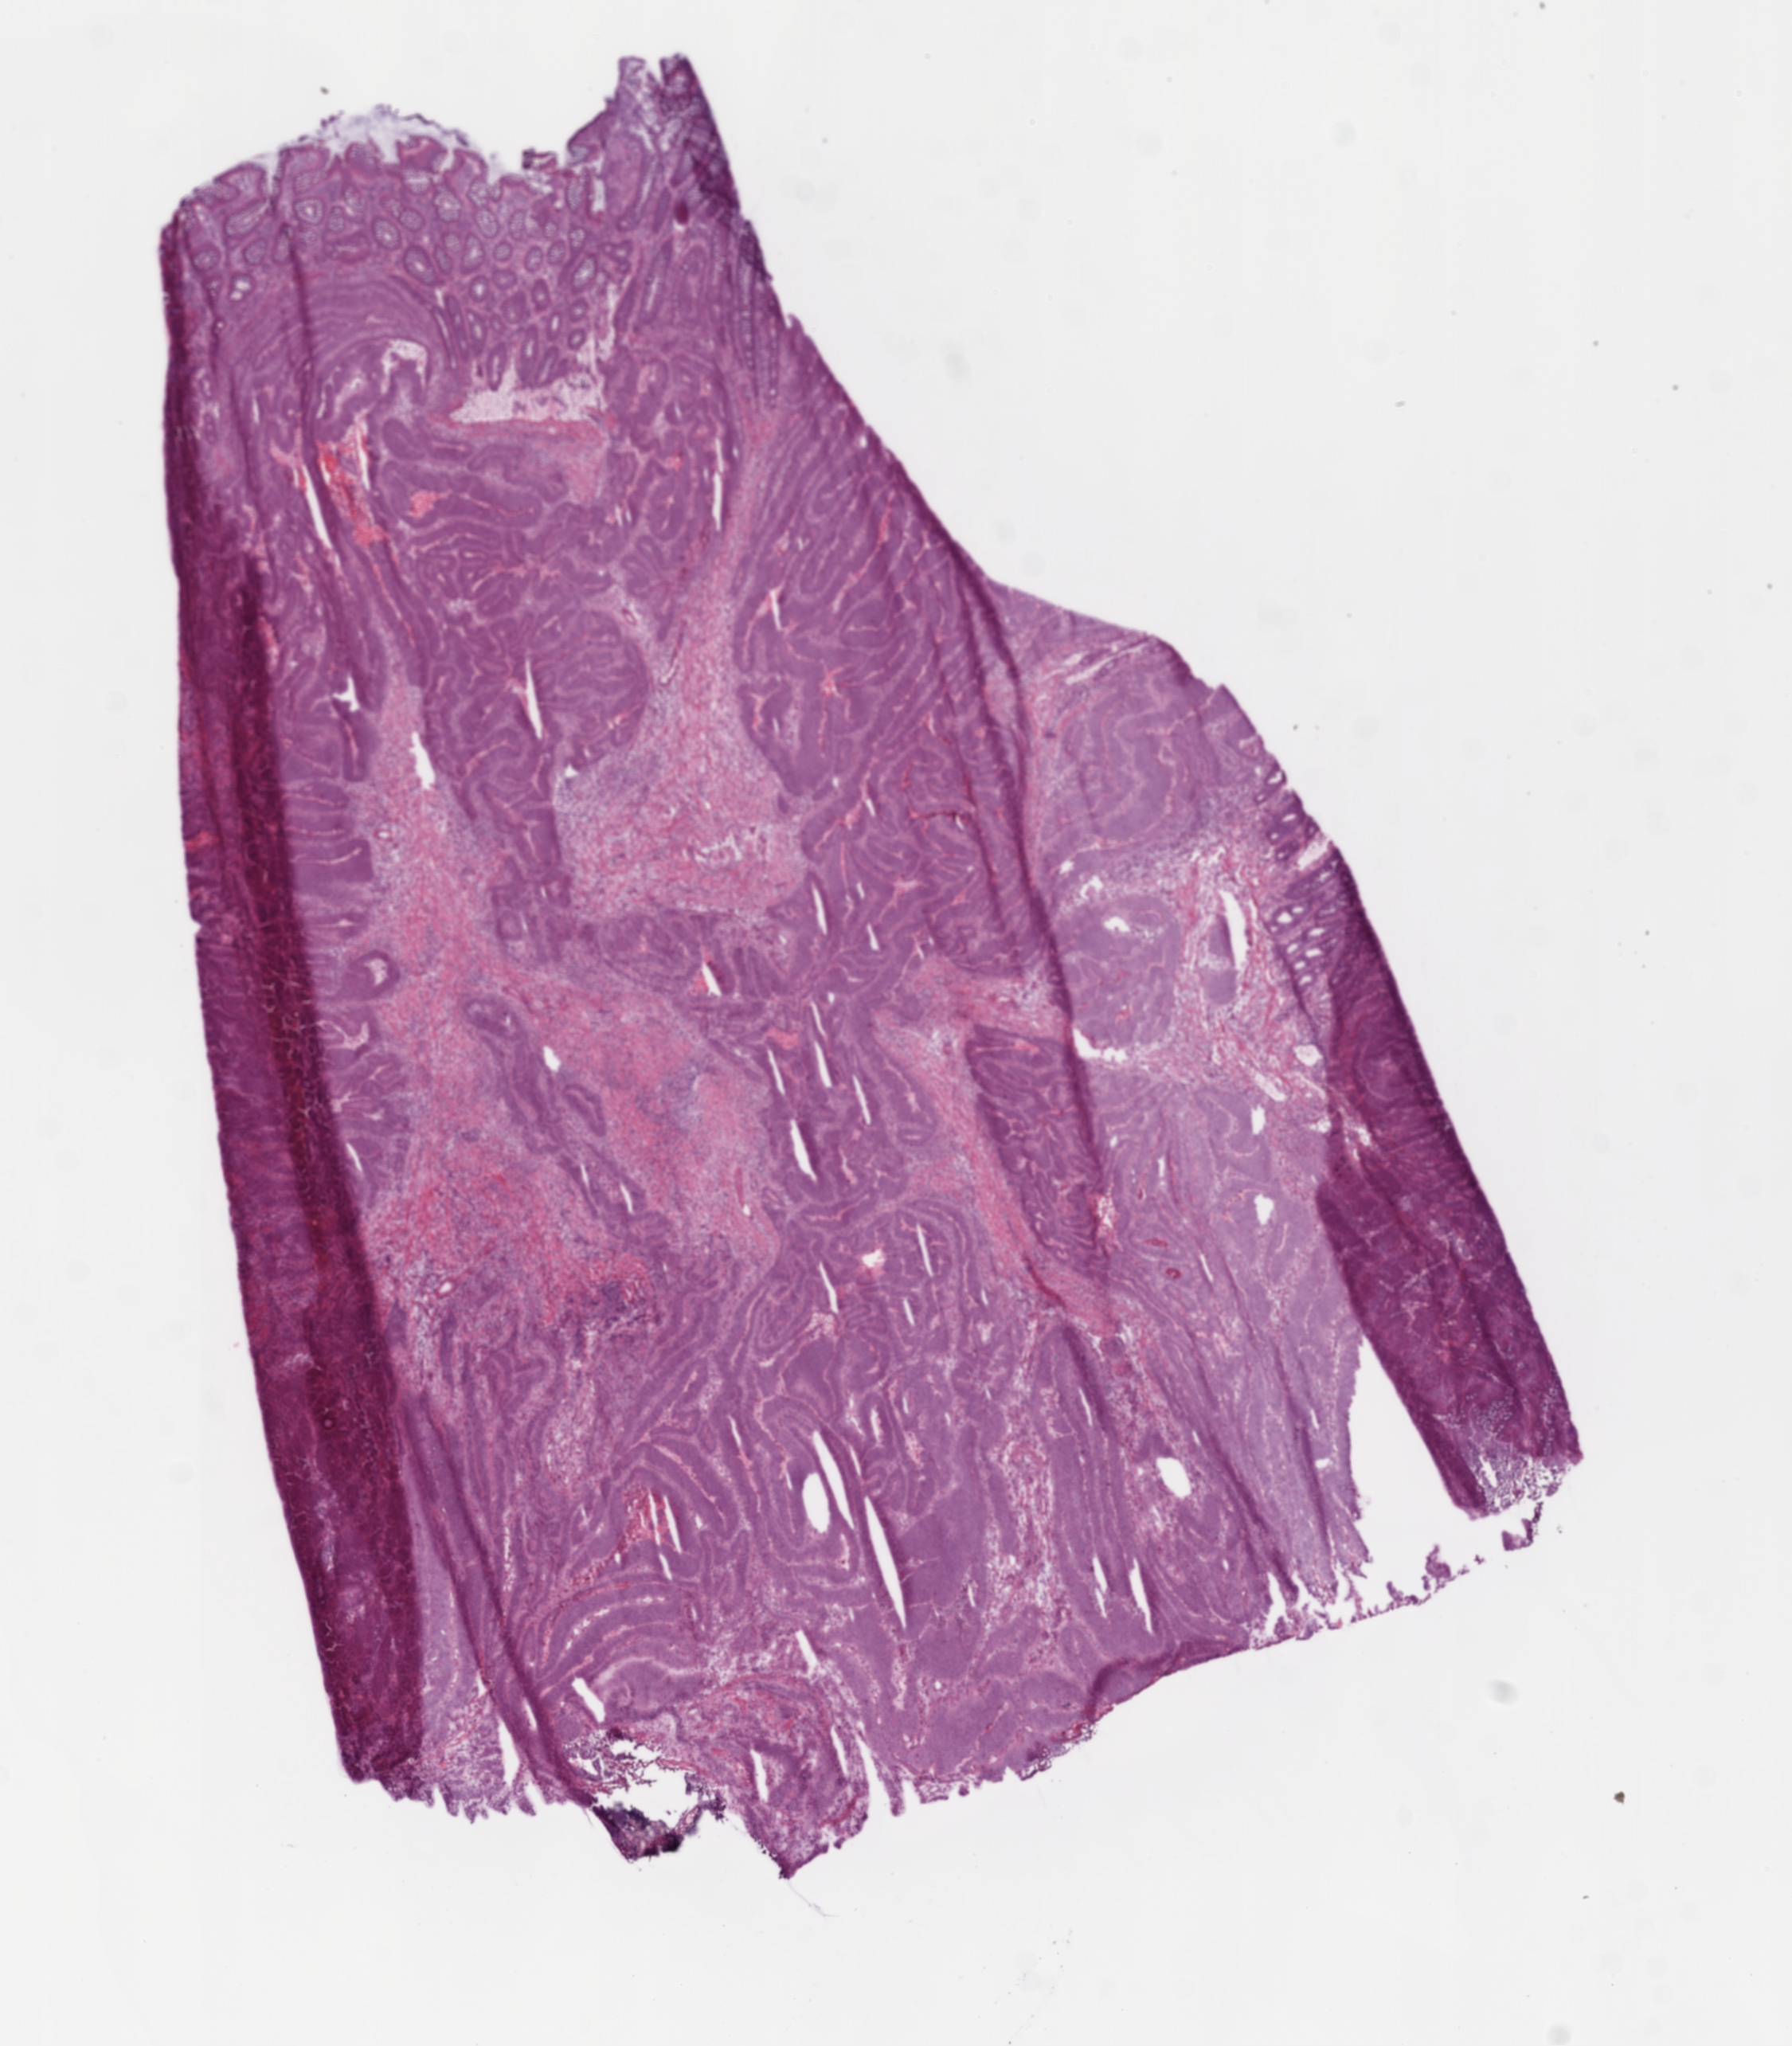
H&E whole-slide image — shown as a low-resolution overview of the whole scanned area (about 9.0 x 10.3 mm, slide scanned at 20x); frozen section from the bottom of the tissue portion; primary tumour sample from the colon. Female, age 60 years at initial diagnosis.
Histologic diagnosis: Adenocarcinoma, NOS (sigmoid colon).